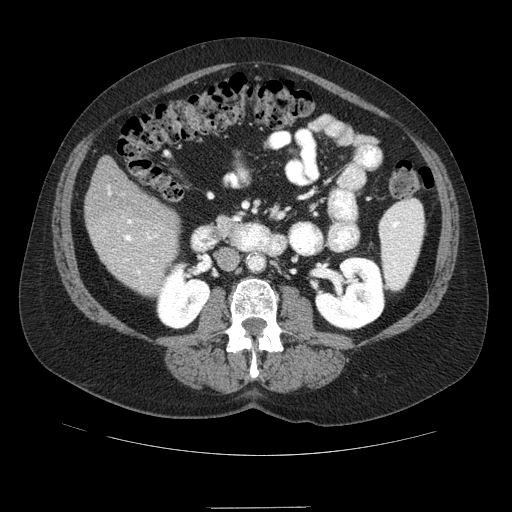
Contrast-enhanced abdominal CT (liver protocol), one axial slice. Slice 25 of 89 in the series (ordered by position). Soft-tissue window (W 400 / L 40 HU). 2.5 mm slice thickness. 512 × 512 image matrix, field of view 400 × 400 mm. Case-level facts recorded for this patient, not image findings: diagnosis: hepatocellular carcinoma (patient treated with transarterial chemoembolisation; whether this scan precedes or follows treatment is not stated here); TNM stage (as recorded): Stage-IIIB; Child-Pugh class: A; tumour nodularity: multinodular.
Outlined on this slice (semi-automatic segmentation, software-assisted and operator-edited):
- liver parenchyma outside the tumour (the mass and vessels are separate outlines, so this box may not span the whole liver): bounding box (x1, y1, x2, y2) in pixels: (85, 156, 178, 294)
- liver vessels: (108, 186, 158, 274)